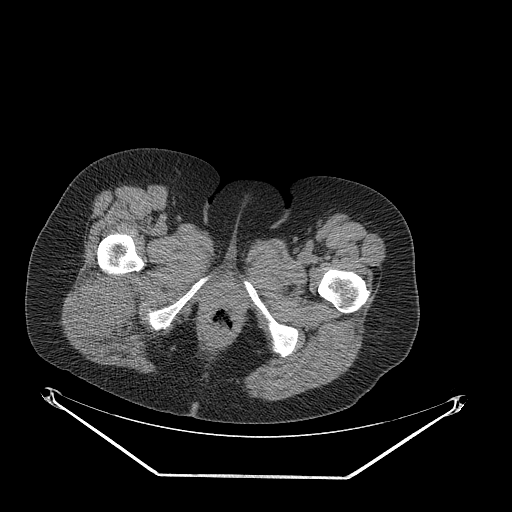
CT of an extremity soft-tissue mass (from a PET/CT study), one axial slice. Slice 56 of 257 in the series (ordered by position). Soft-tissue window (W 400 / L 40 HU). 3.75 mm slice thickness. 512 × 512 image matrix, field of view 500 × 500 mm. Female patient. Case-level facts recorded for this patient, not image findings: histological type: synovial sarcoma; grade: intermediate; site of the primary tumour: right buttock.
Structures marked on this image (expert contour drawn on MRI and transferred to this co-registered scan by the dataset authors):
- gross tumour volume including surrounding oedema: bounding box (x1, y1, x2, y2) in pixels: (78, 269, 140, 352)
- gross tumour volume (mass): (78, 269, 140, 341)